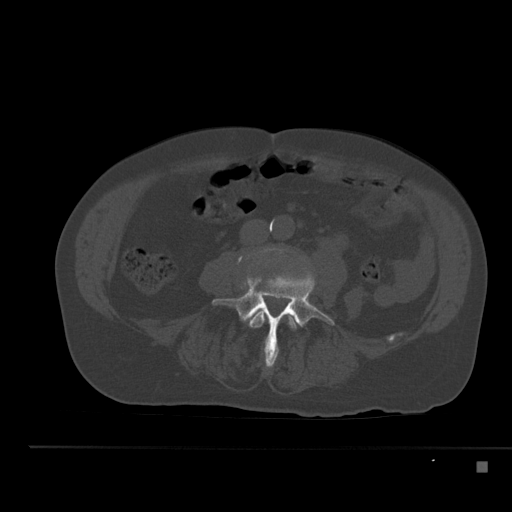
CT including the spine, one axial slice; position 148 of 517 along the scan axis; reconstruction kernel Br40s; 120 kVp; bone window (W 1800 / L 400 HU); 1.5 mm slice thickness; 512 × 512 image matrix, field of view 408 × 408 mm. Patient: male, 70 years. From the clinical record (not read from this slice): primary cancer: renal; vertebrae with lytic lesions (as recorded): T4, T6, T10, T12, L3, L4, L5.
Annotated regions visible in this slice (semi-automatic segmentation, software-assisted and operator-edited):
- L3 vertebra: bounding box [x1, y1, x2, y2] px = [248, 263, 298, 365]
- L4 vertebra: [212, 257, 335, 367]